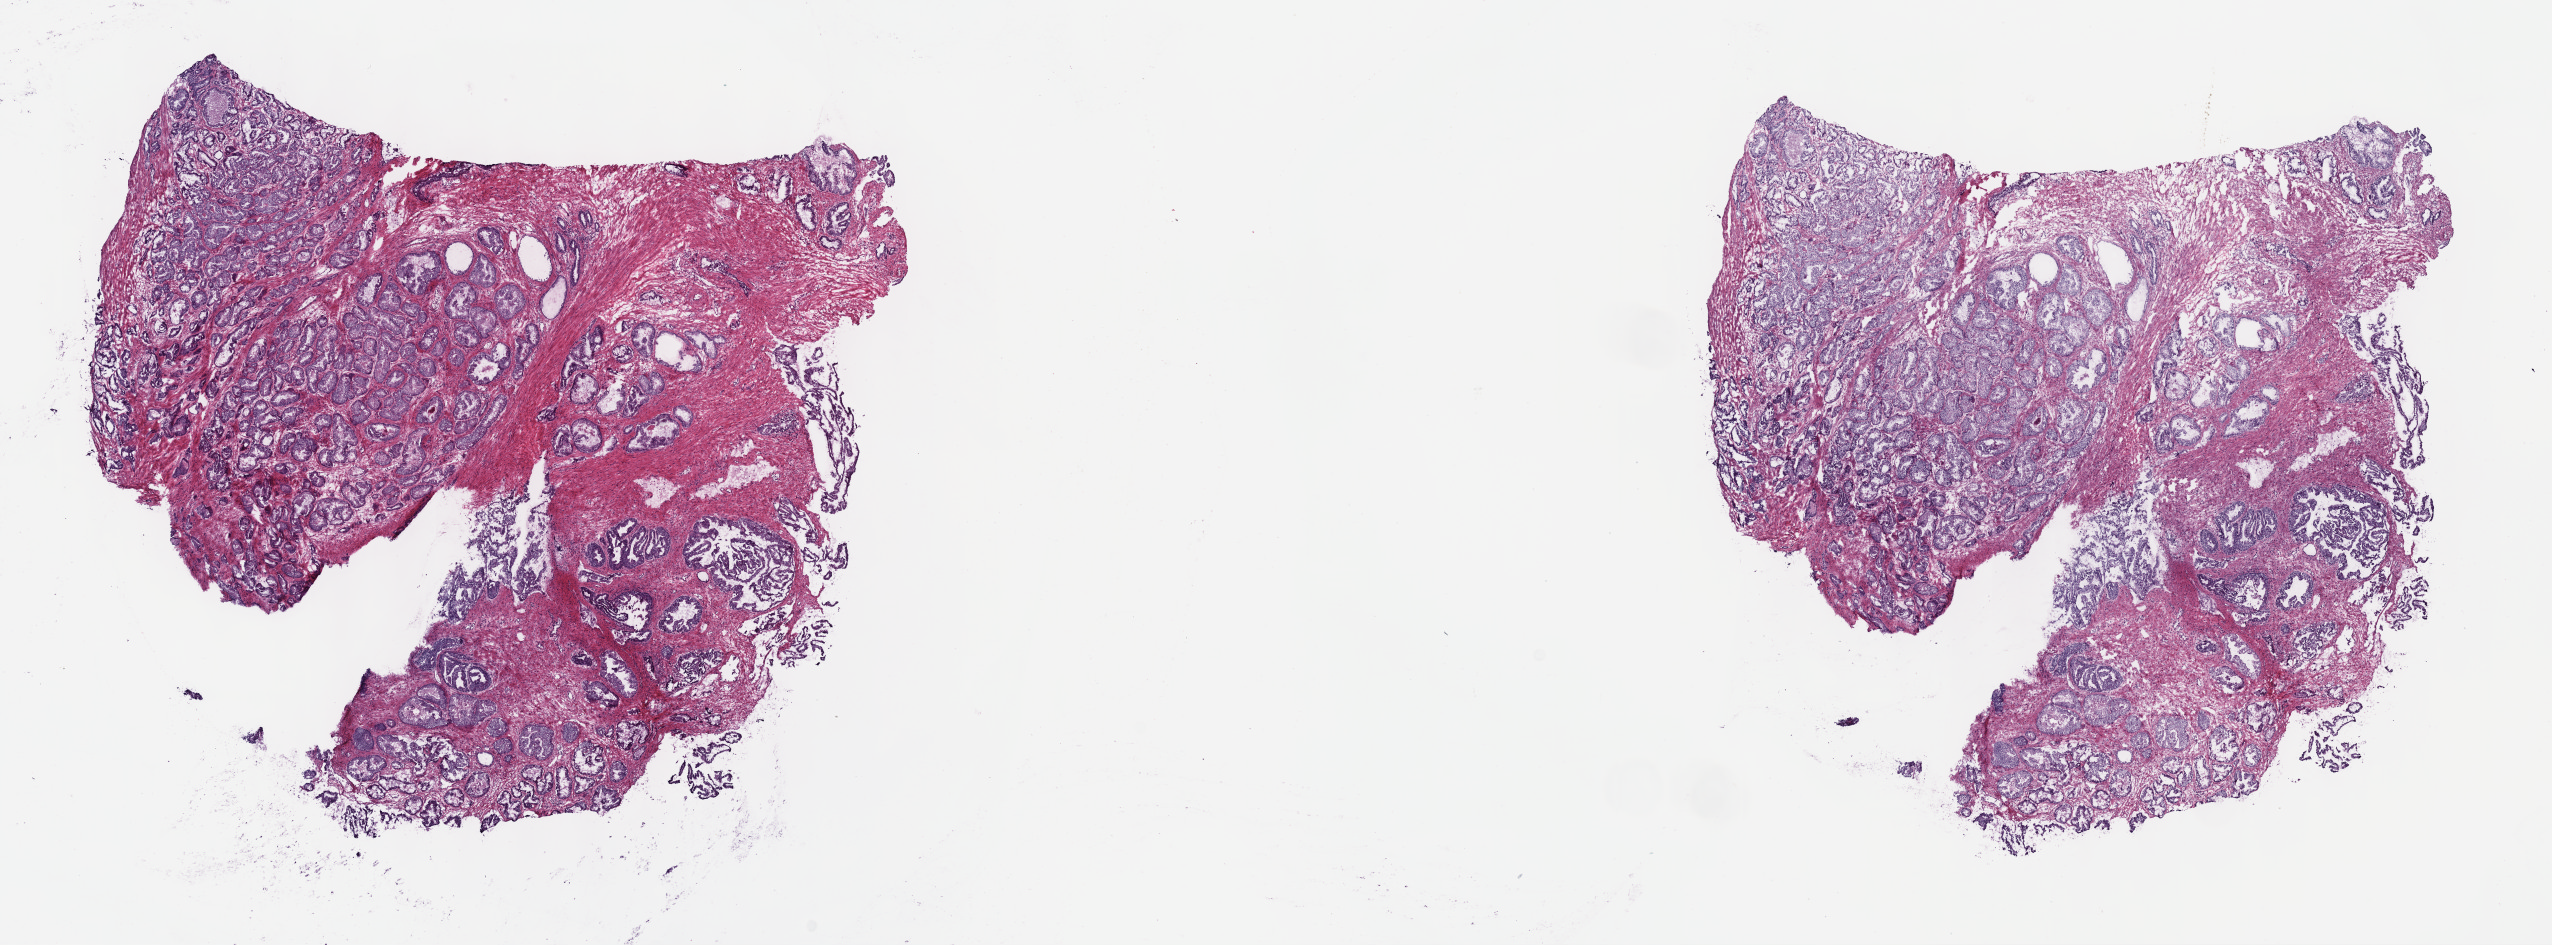
Digitized Hematoxylin and eosin (H&E) stained tissue section (whole slide) — a low-resolution overview of the entire scanned area, about 20.6 x 7.6 mm (slide scanned at 40x), frozen section from the top of the tissue portion, prostate, primary tumour sample. Patient: male, age at initial diagnosis 61 years.
Histologic diagnosis: Adenocarcinoma, NOS (prostate gland).